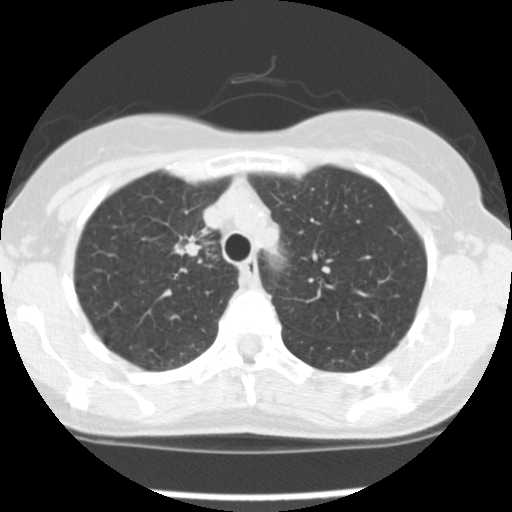
Low-dose screening chest CT, one axial slice. Slice 119 of 157 in the series (ordered by position). Reconstruction kernel STANDARD. 120 kVp. Lung window (W 1500 / L -600 HU). 512 × 512 image matrix, field of view 282 × 282 mm.
Structures marked on this image (manually delineated by an expert):
- lesion 1 (tumor, upper lobe of right lung): bounding box <174,235,206,257> (left, top, right, bottom; pixels)